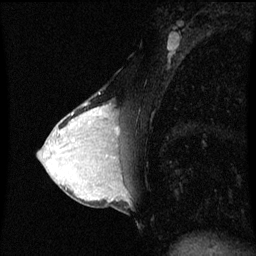
Breast MRI (dynamic contrast-enhanced), one sagittal slice; slice 34 of 60 in the series (ordered by position); dynamic contrast-enhanced series, image 2 of 3 at this slice position (ordered by acquisition); 1.5 T; TE 4.2 ms, TR 8.9 ms; 2 mm slice thickness; 256 × 256 image matrix, field of view 200 × 200 mm. Female patient, age 33 years. From the clinical record (not read from this slice): setting: breast cancer imaged before/during neoadjuvant chemotherapy; receptor status: HER2-positive.
Annotated regions visible in this slice (semi-automatic segmentation, software-assisted and operator-edited):
- analysis volume of interest (the breast-tissue region the enhancement analysis was run in; not a lesion): bounding box <95,106,124,153> (left, top, right, bottom; pixels)
- tumour enhancement mask (voxels above the 70 % enhancement threshold inside the analysis volume of interest): <116,128,118,135>